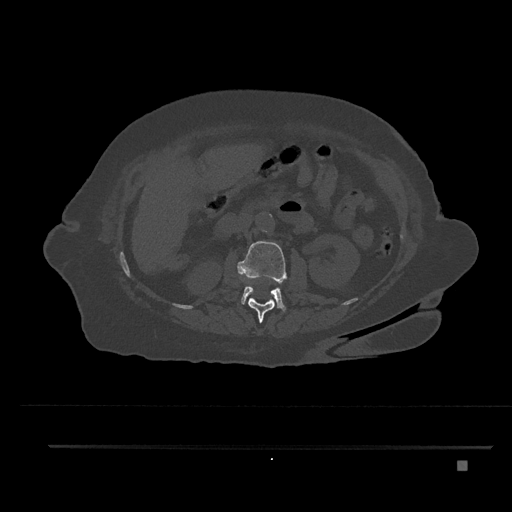
CT including the spine, one axial slice. Slice 200 of 797 in the series (ordered by position). Bone window (W 1800 / L 400 HU). 0.5 mm slice thickness. 512 × 512 image matrix. Patient: female, 76 years. Case-level facts recorded for this patient, not image findings: primary cancer: lung.
Annotated regions visible in this slice (semi-automatic segmentation, software-assisted and operator-edited):
- L1 vertebra: bounding box [x1, y1, x2, y2] px = [248, 298, 276, 323]
- L2 vertebra: [237, 241, 287, 311]